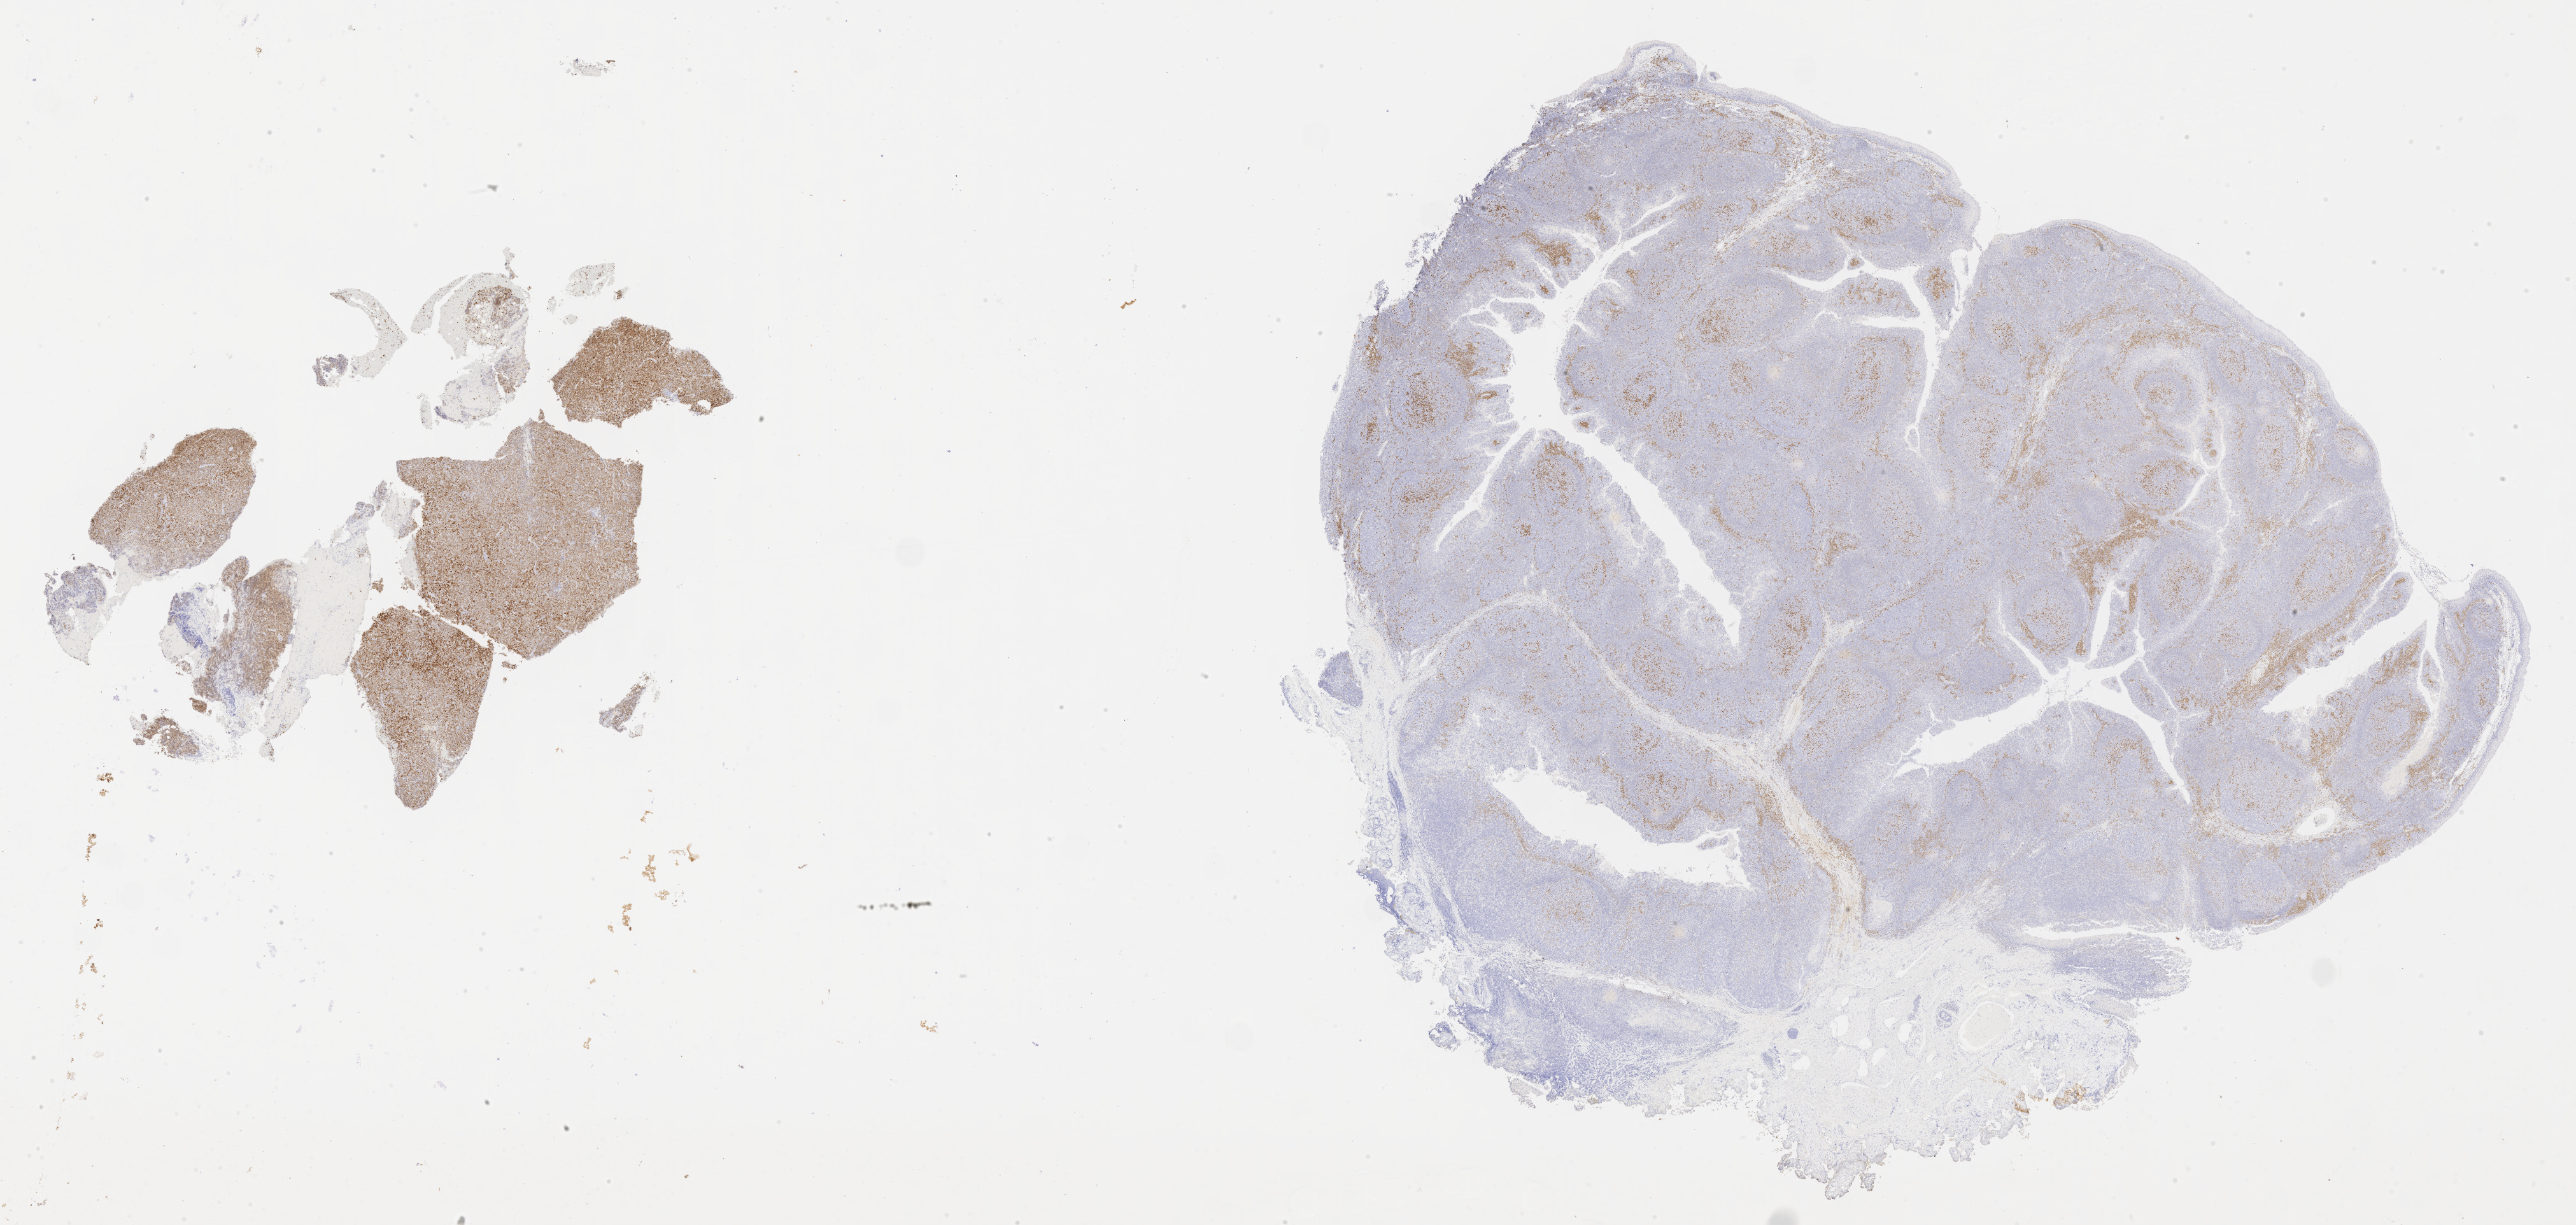
Whole-slide image, immunohistochemical stain for IRF4/MUM1, shown as a low-resolution overview of the whole scanned area (about 32.7 x 15.6 mm); tumor tissue; site: lymph node. Female patient, aged 71.
• diagnosis: Diffuse large B-cell lymphoma, NOS